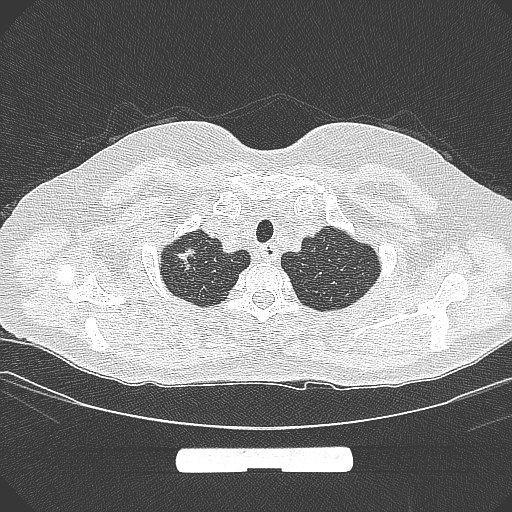
Chest CT, one axial slice; slice 264 of 295 in the series (ordered by position); 120 kVp; lung window (W 1500 / L -600 HU); 1 mm slice thickness; 512 × 512 image matrix, field of view 369 × 369 mm. Patient: female, 58 years. From the clinical record (not read from this slice): clinical TNM (as recorded): T1b N0 M0.
Outlined on this slice (bounding box drawn by a radiologist):
- lung tumour (recorded histology: adenocarcinoma): bounding box [x1, y1, x2, y2] px = [172, 245, 201, 277]